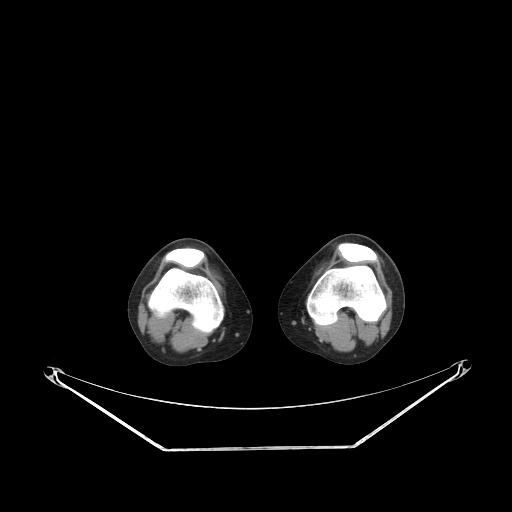
CT of an extremity soft-tissue mass (from a PET/CT study), one axial slice. Position 164 of 223 along the scan axis. Reconstruction kernel STANDARD. 140 kVp. Soft-tissue window (W 400 / L 40 HU). 3.75 mm slice thickness. 512 × 512 image matrix, field of view 500 × 500 mm. Female patient. Case-level facts recorded for this patient, not image findings: histological type: spindle cell suggestive of biphasic synovial sarcoma; grade: intermediate; site of the primary tumour: left knee.
Annotated regions visible in this slice (expert contour drawn on MRI and transferred to this co-registered scan by the dataset authors):
- gross tumour volume including surrounding oedema: bounding box [x1, y1, x2, y2] px = [379, 281, 389, 295]